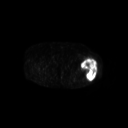
FDG PET of an extremity soft-tissue mass (from a PET/CT study), one axial slice; slice 240 of 267 in the series (ordered by position); 128 × 128 image matrix, field of view 700 × 700 mm. Patient: female, 62 years. From the clinical record (not read from this slice): histological type: undifferentiated – high grade; grade: high; site of the primary tumour: left thigh.
Structures marked on this image (expert contour drawn on MRI and transferred to this co-registered scan by the dataset authors):
- gross tumour volume including surrounding oedema: bounding box [x1, y1, x2, y2] px = [81, 58, 98, 81]
- gross tumour volume (mass): [81, 58, 98, 81]